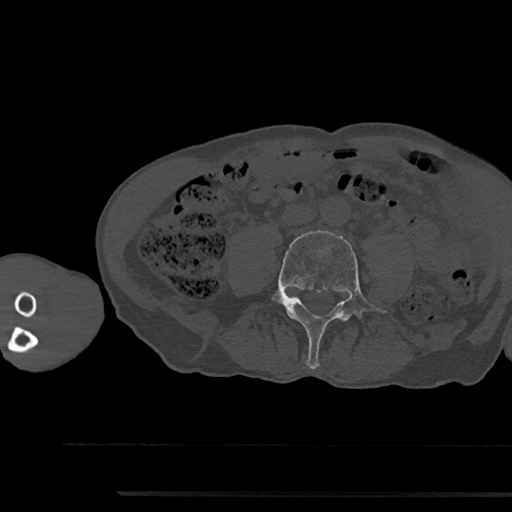
CT including the spine, one axial slice. Position 412 of 797 along the scan axis. 120 kVp. Bone window (W 1800 / L 400 HU). 512 × 512 image matrix, field of view 367 × 367 mm. Male patient, age 79 years. From the clinical record (not read from this slice): primary cancer: prostate.
Outlined on this slice (semi-automatically segmented with operator editing):
- L4 vertebra: bounding box <273,231,391,369> (left, top, right, bottom; pixels)